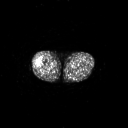
FDG PET of an extremity soft-tissue mass (from a PET/CT study), one axial slice; slice 226 of 267 in the series (ordered by position); 3.27 mm slice thickness; 128 × 128 image matrix, field of view 700 × 700 mm. Male patient, age 43 years. Case-level facts recorded for this patient, not image findings: histological type: poorly differentiated synovial sarcoma; grade: high; site of the primary tumour: right buttock.
Structures marked on this image (expert contour drawn on MRI and transferred to this co-registered scan by the dataset authors):
- gross tumour volume including surrounding oedema: bounding box (x1, y1, x2, y2) in pixels: (34, 59, 43, 68)